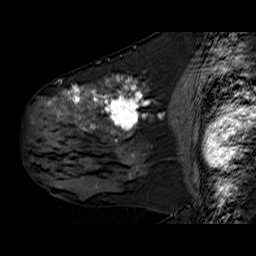
Breast MRI (dynamic contrast-enhanced), one sagittal slice; slice 33 of 60 in the series (ordered by position); dynamic contrast-enhanced series, time point 2 of 6 at this slice position (early post-contrast); 1.5 T; TE 6.3 ms, TR 32.9 ms; 4 mm slice thickness; 256 × 256 image matrix, field of view 200 × 200 mm. Female patient. From the clinical record (not read from this slice): setting: breast cancer imaged before/during neoadjuvant chemotherapy; receptor status: HER2-positive.
Outlined on this slice (semi-automatic segmentation, software-assisted and operator-edited):
- analysis volume of interest (the breast-tissue region the enhancement analysis was run in; not a lesion): bounding box [x1, y1, x2, y2] px = [30, 78, 172, 180]
- tumour enhancement mask (voxels above the 100 % enhancement threshold inside the analysis volume of interest): [48, 78, 150, 177]